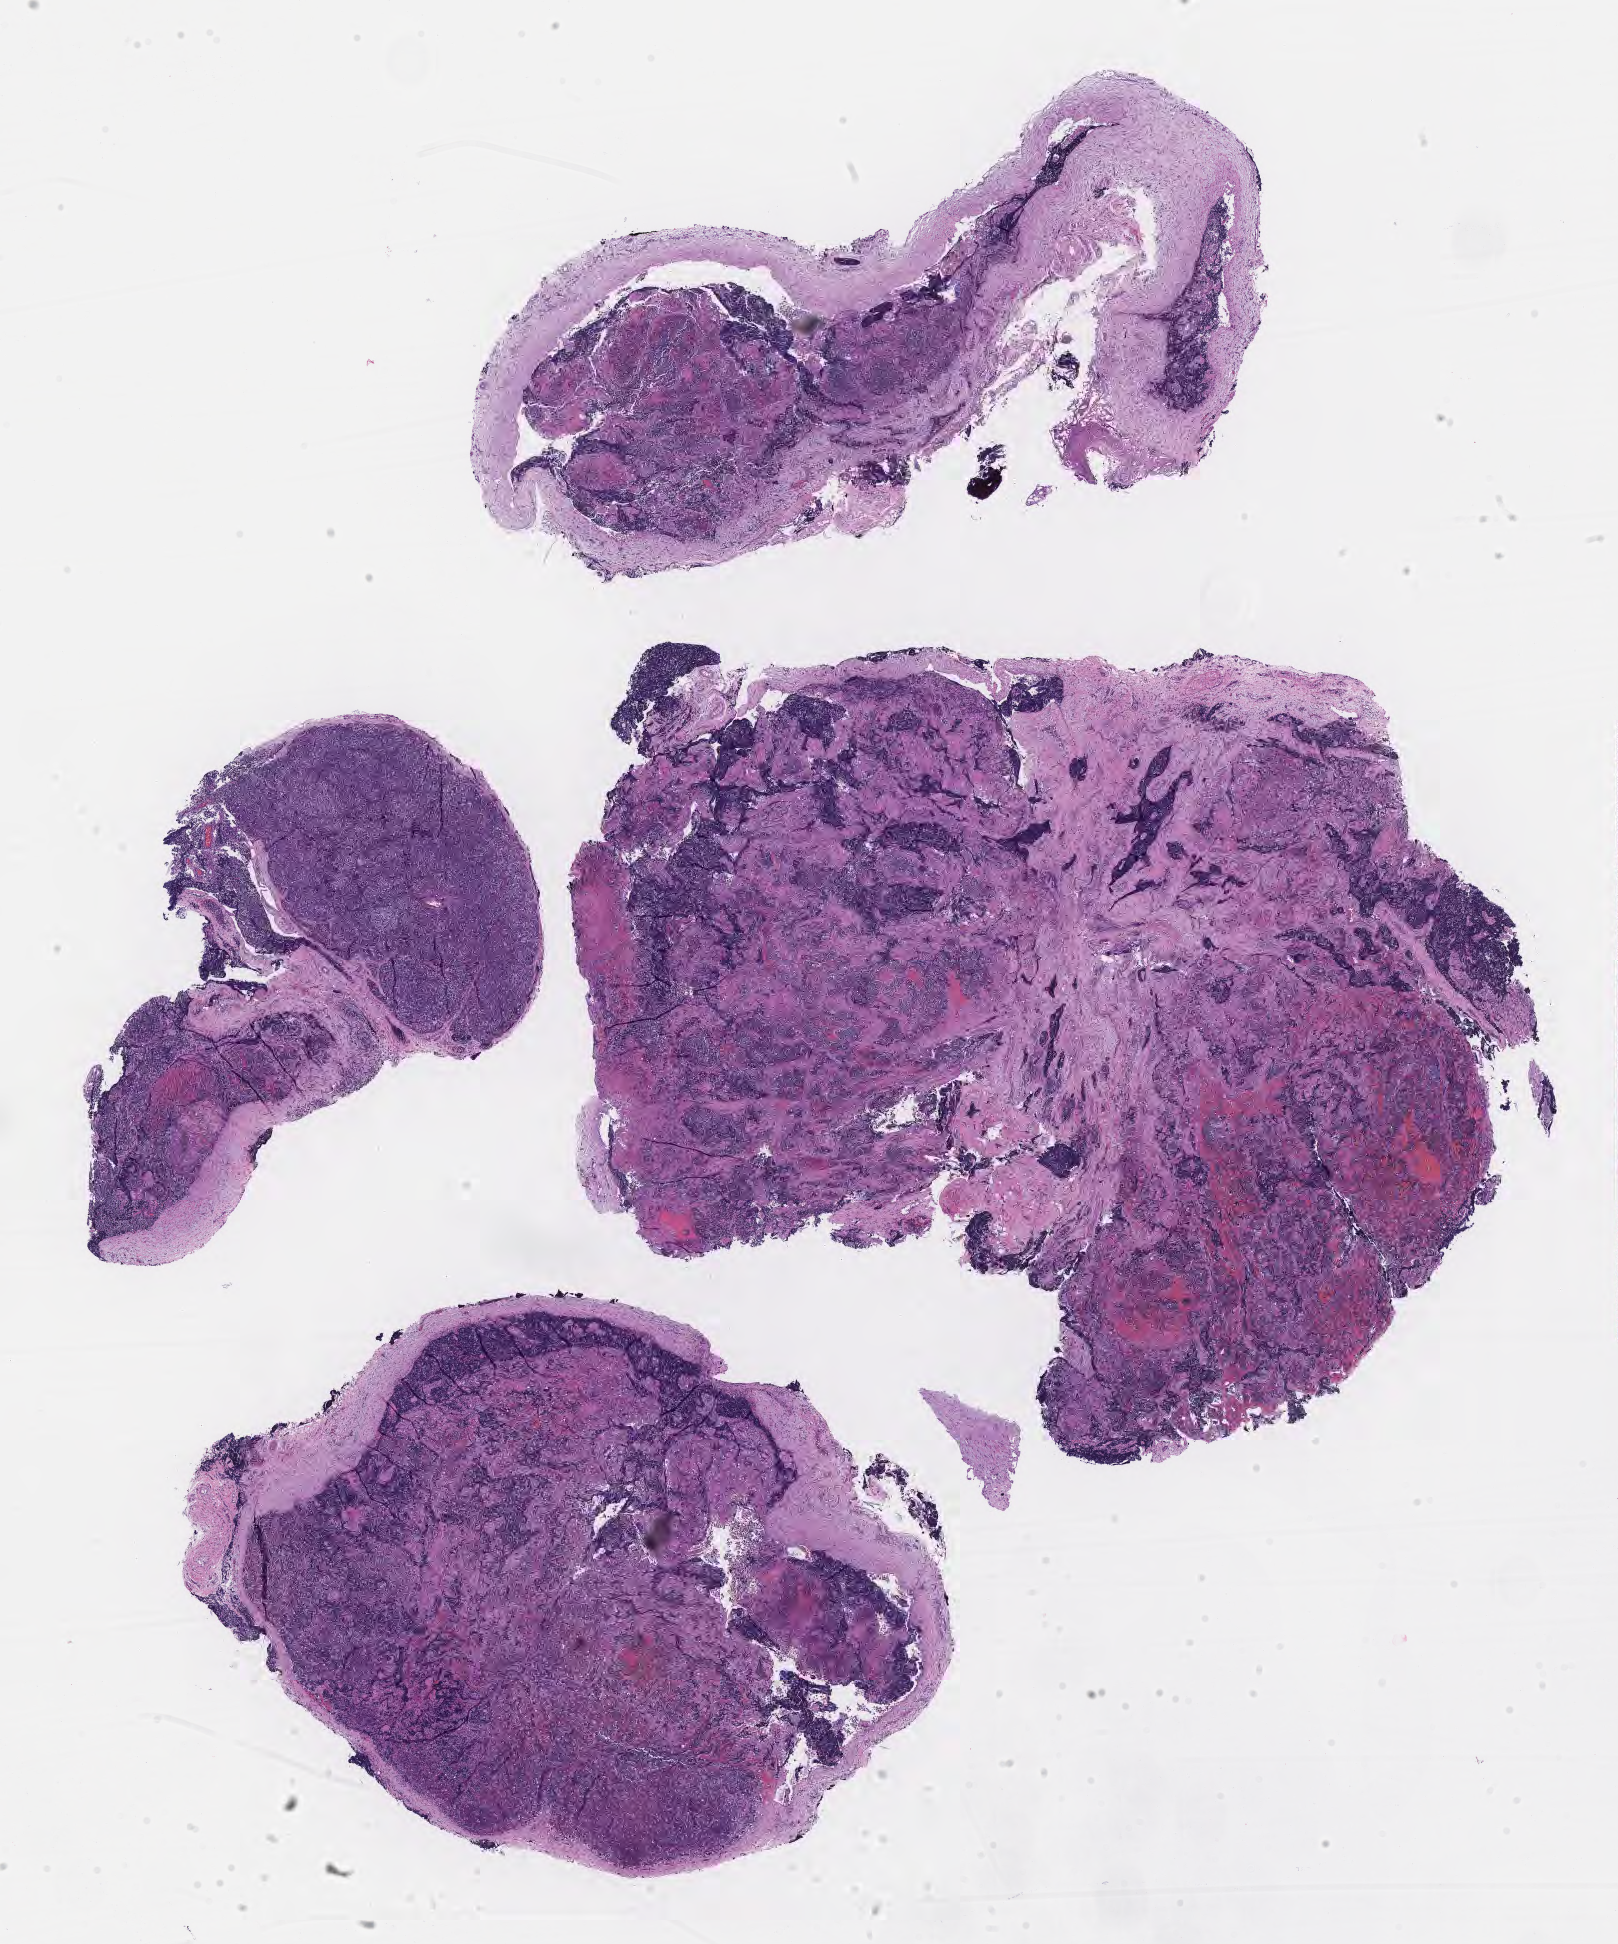
Whole-slide image, H&E stain of tumor tissue from the head and neck lymph node, low-resolution overview of the scanned area, about 13.1 x 15.7 mm; FFPE section. Patient: female, age 122 days.
Diagnosis (ICD-O-3 morphology term): Neuroblastoma, NOS.